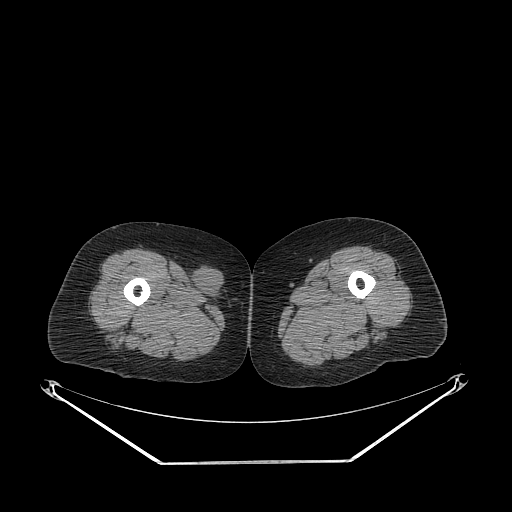
CT of an extremity soft-tissue mass (from a PET/CT study), one axial slice. Position 241 of 311 along the scan axis. Reconstruction kernel STANDARD. Soft-tissue window (W 400 / L 40 HU). 3.75 mm slice thickness. 512 × 512 image matrix, field of view 500 × 500 mm. Female patient. From the clinical record (not read from this slice): histological type: leiomyosarcoma; grade: intermediate; site of the primary tumour: parascapusular.
Outlined on this slice (expert contour drawn on MRI and transferred to this co-registered scan by the dataset authors):
- gross tumour volume including surrounding oedema: bounding box (x1, y1, x2, y2) in pixels: (192, 263, 227, 302)
- gross tumour volume (mass): (196, 263, 225, 295)